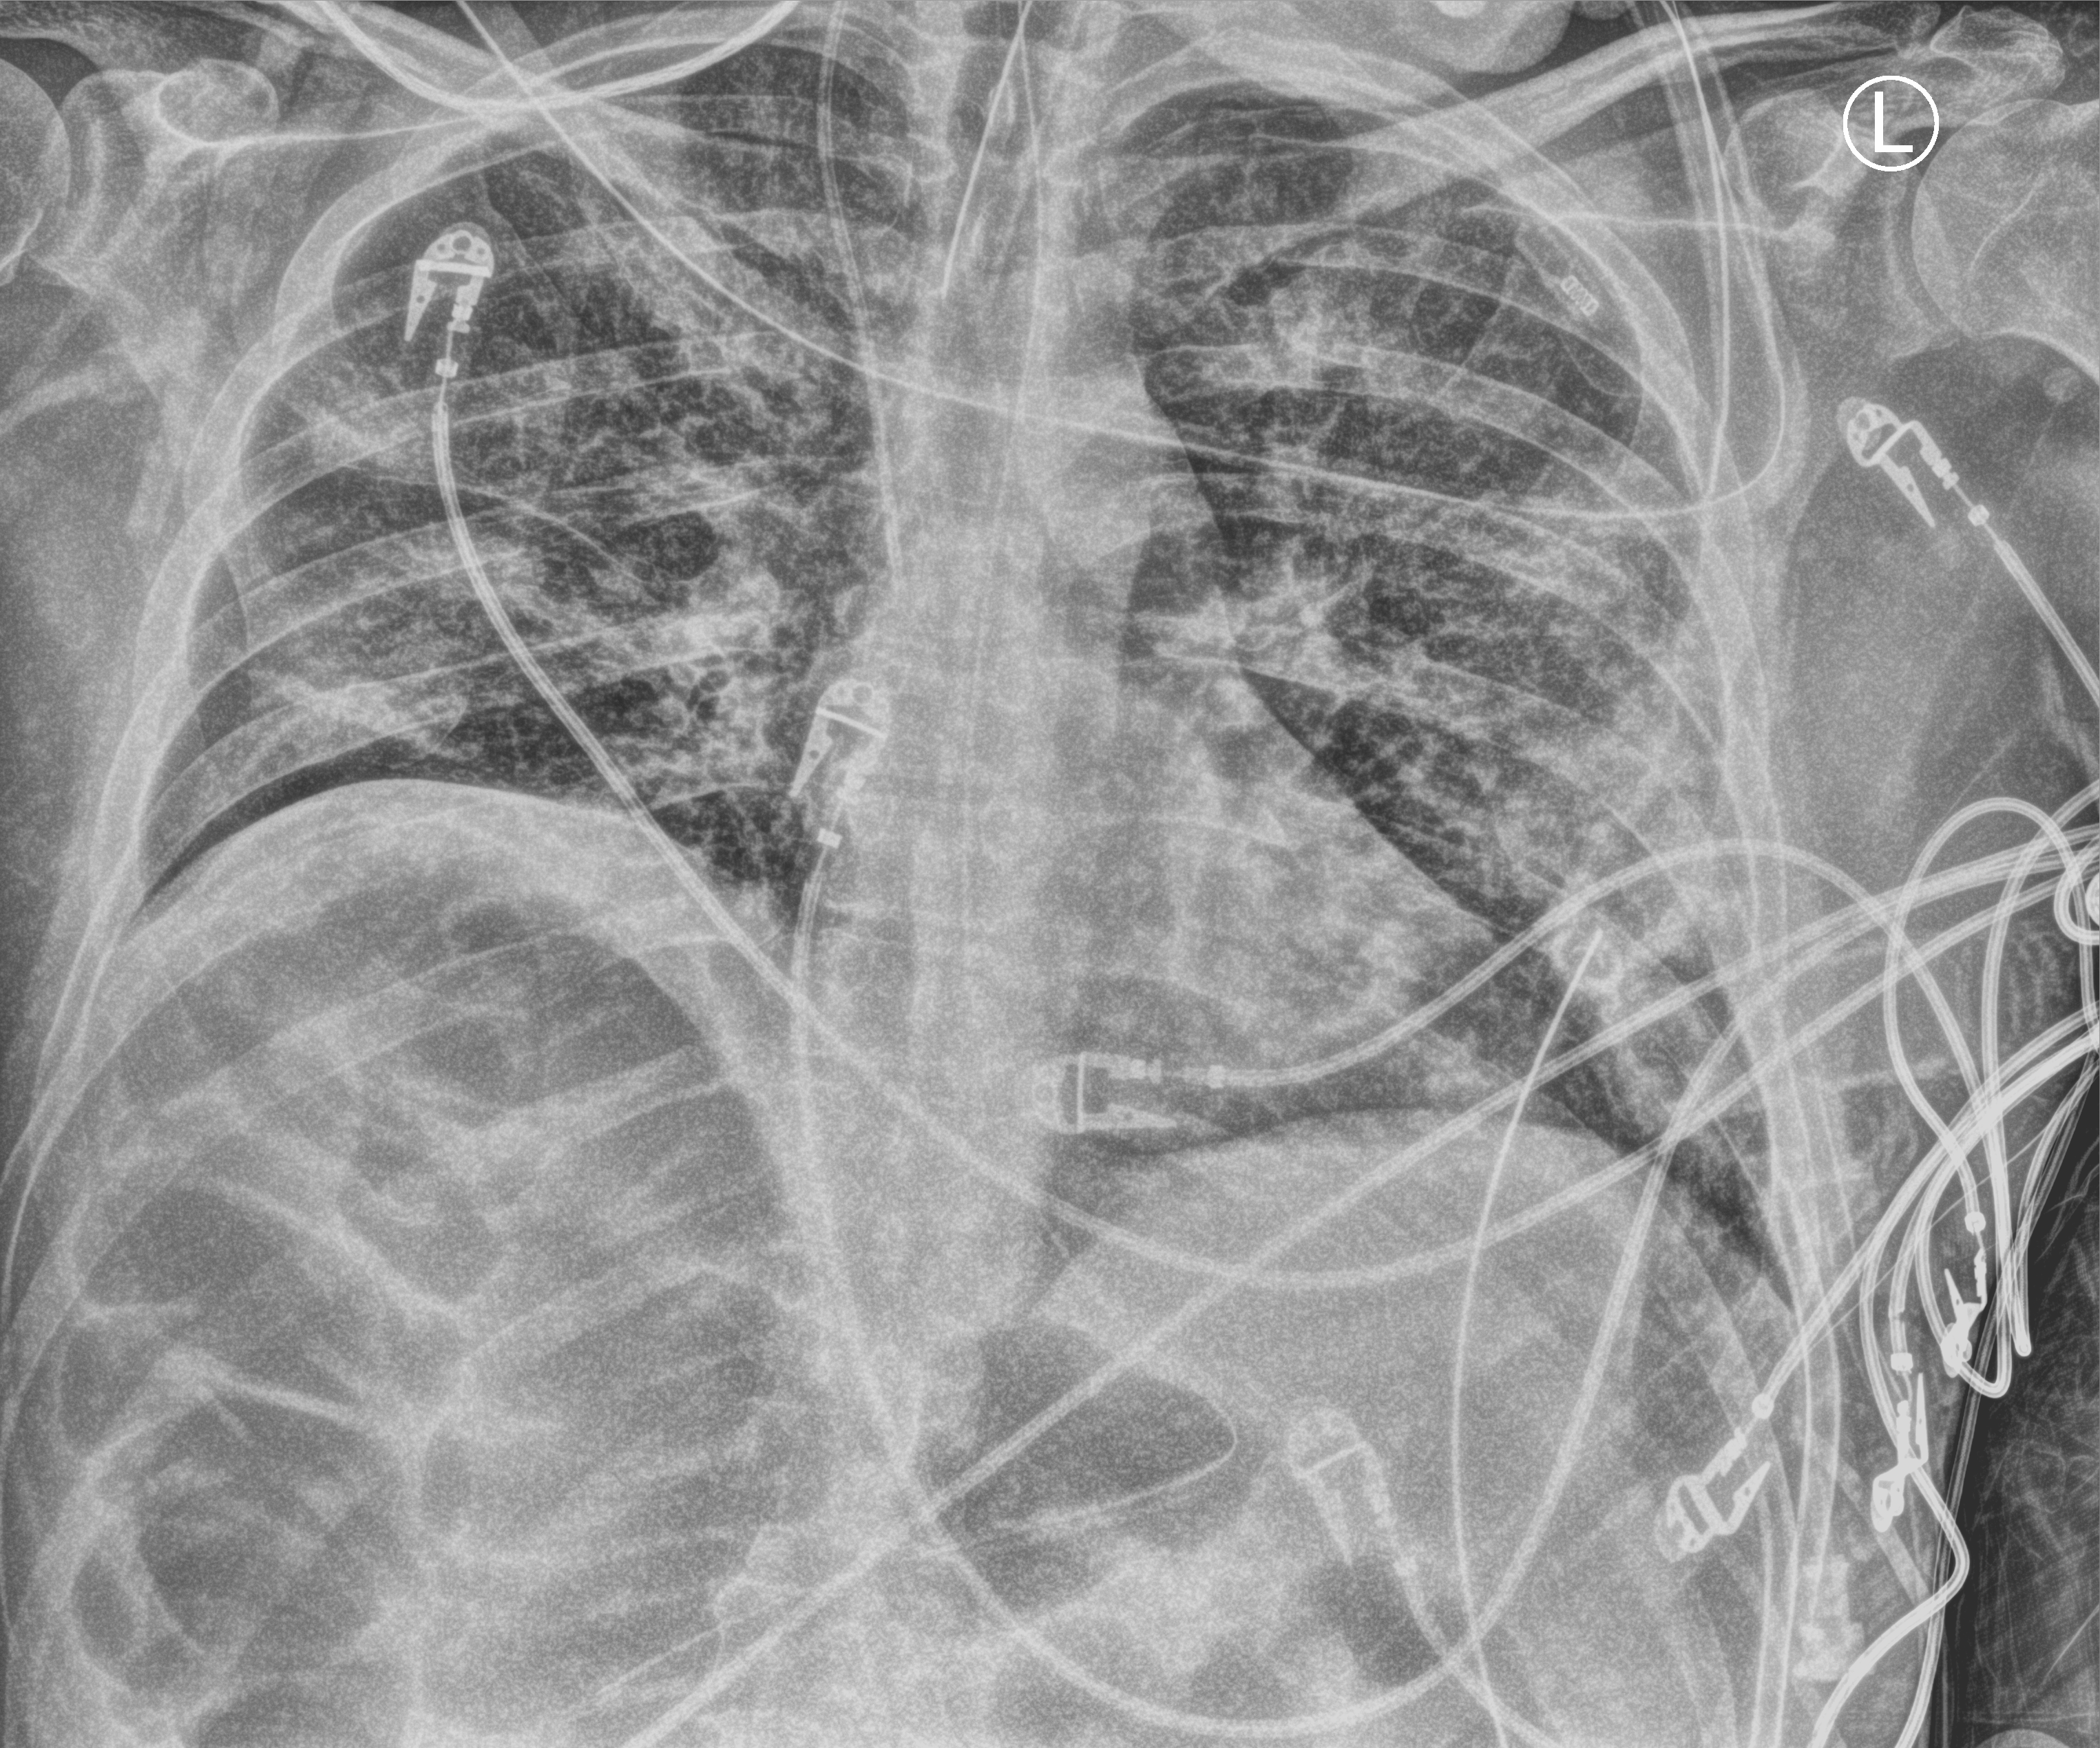
Bedside chest radiograph (computed radiography). Male patient hospitalised with COVID-19, age 18–59 years.
From the hospital-stay record, not from the radiograph (when in the stay this image was taken is not recorded): diabetes (admission record): no; mechanically ventilated during this hospital stay: yes; COPD (admission record): no.